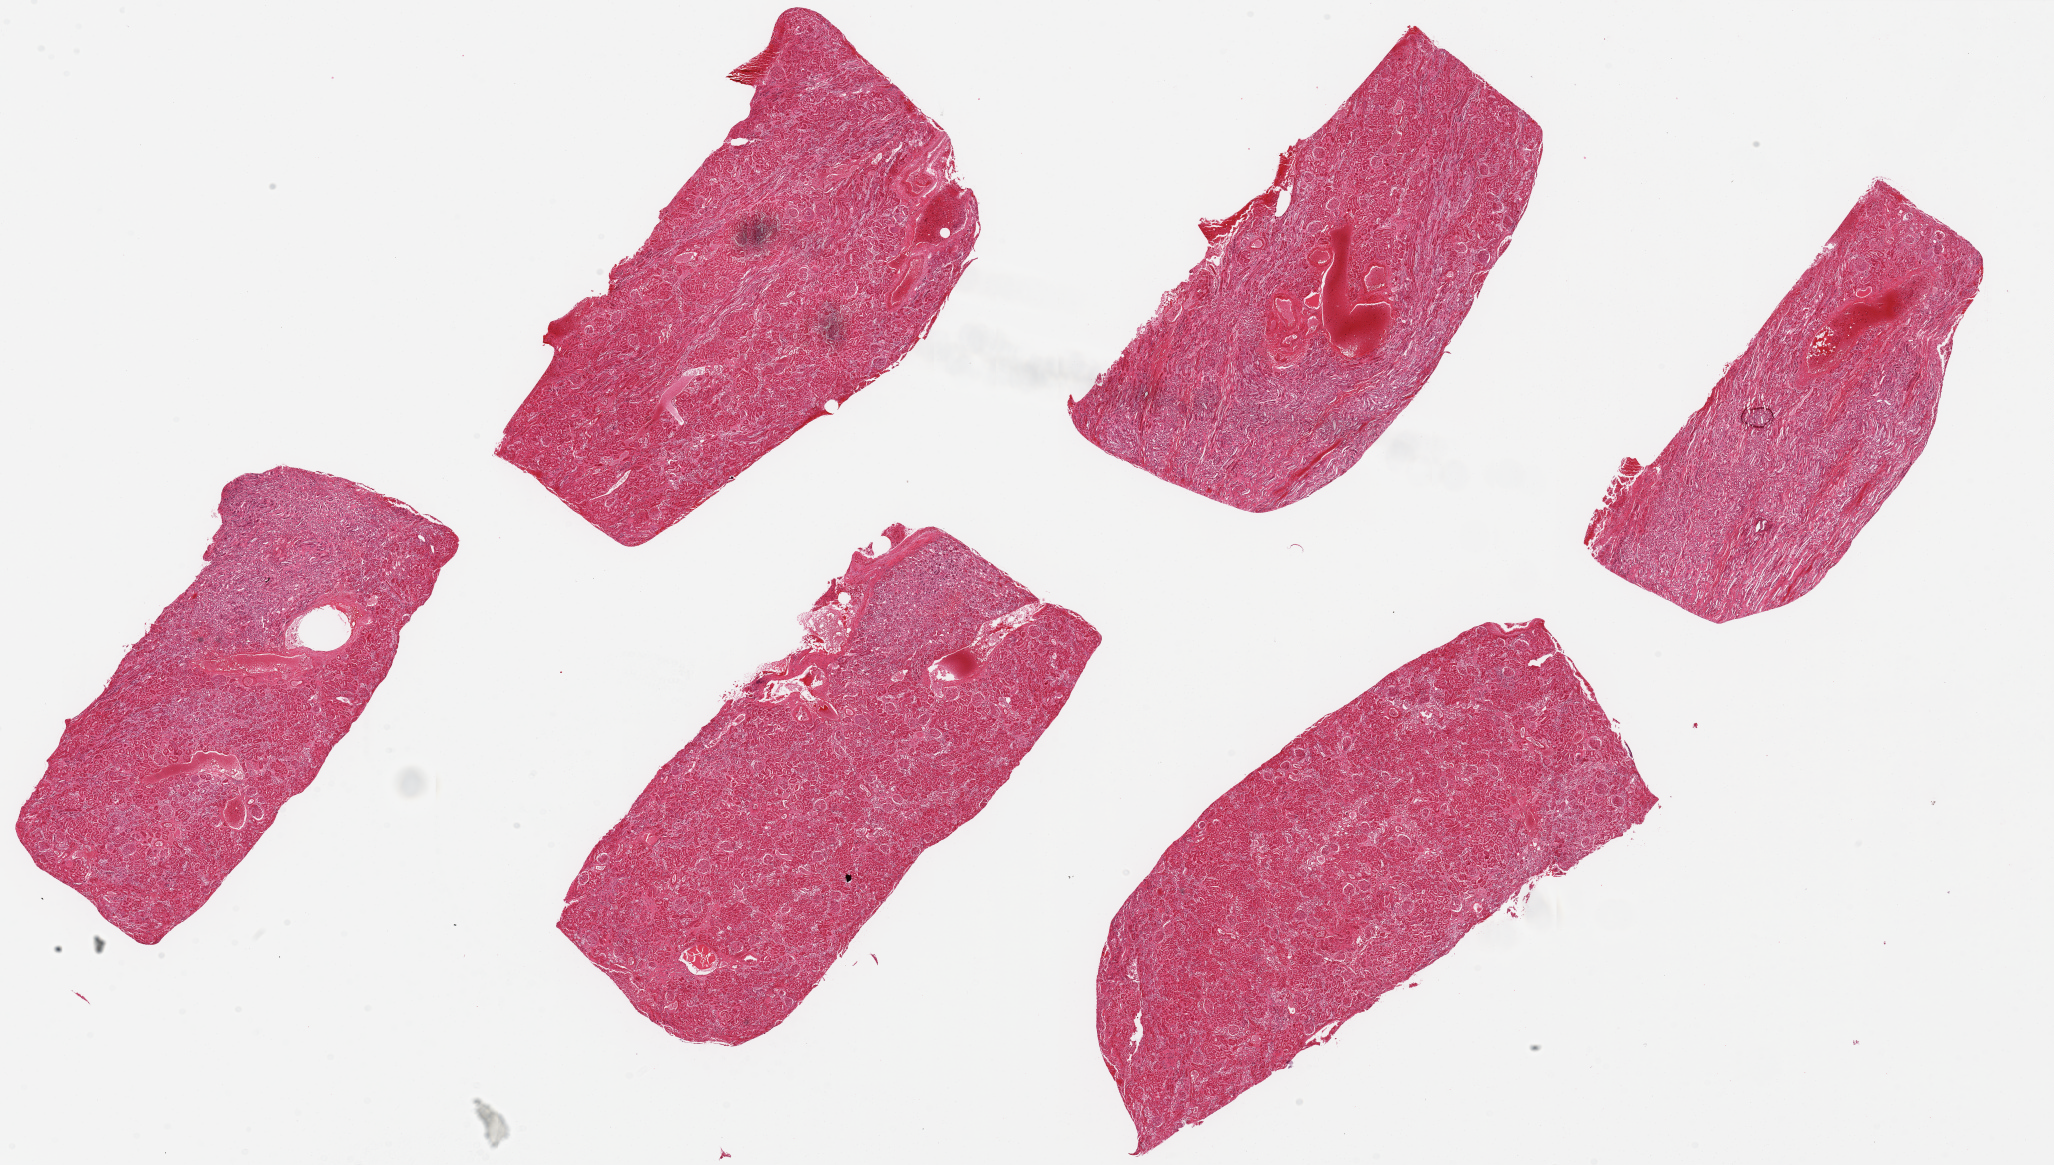
Whole-slide image, hematoxylin and eosin (H&E) stain, brightfield — shown as a low-resolution overview of the whole scanned area (about 32.5 x 18.4 mm, slide scanned at 20x). PAXgene-fixed paraffin-embedded (PFPE) section. Target tissue: renal cortex. Tissue donor sample. Female donor.
* reviewer comment on this tissue sample: 6 ~8x3.5mm pieces, marked tubular autolysis